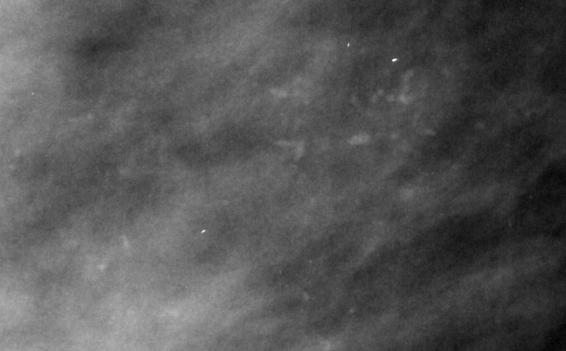
Cropped region of a digitized screen-film mammogram centred on a radiologist-marked abnormality, left breast, MLO view.
Calcifications, morphology pleomorphic, distribution linear; BI-RADS assessment category 4; pathology result (as recorded, not read from the image): malignant.